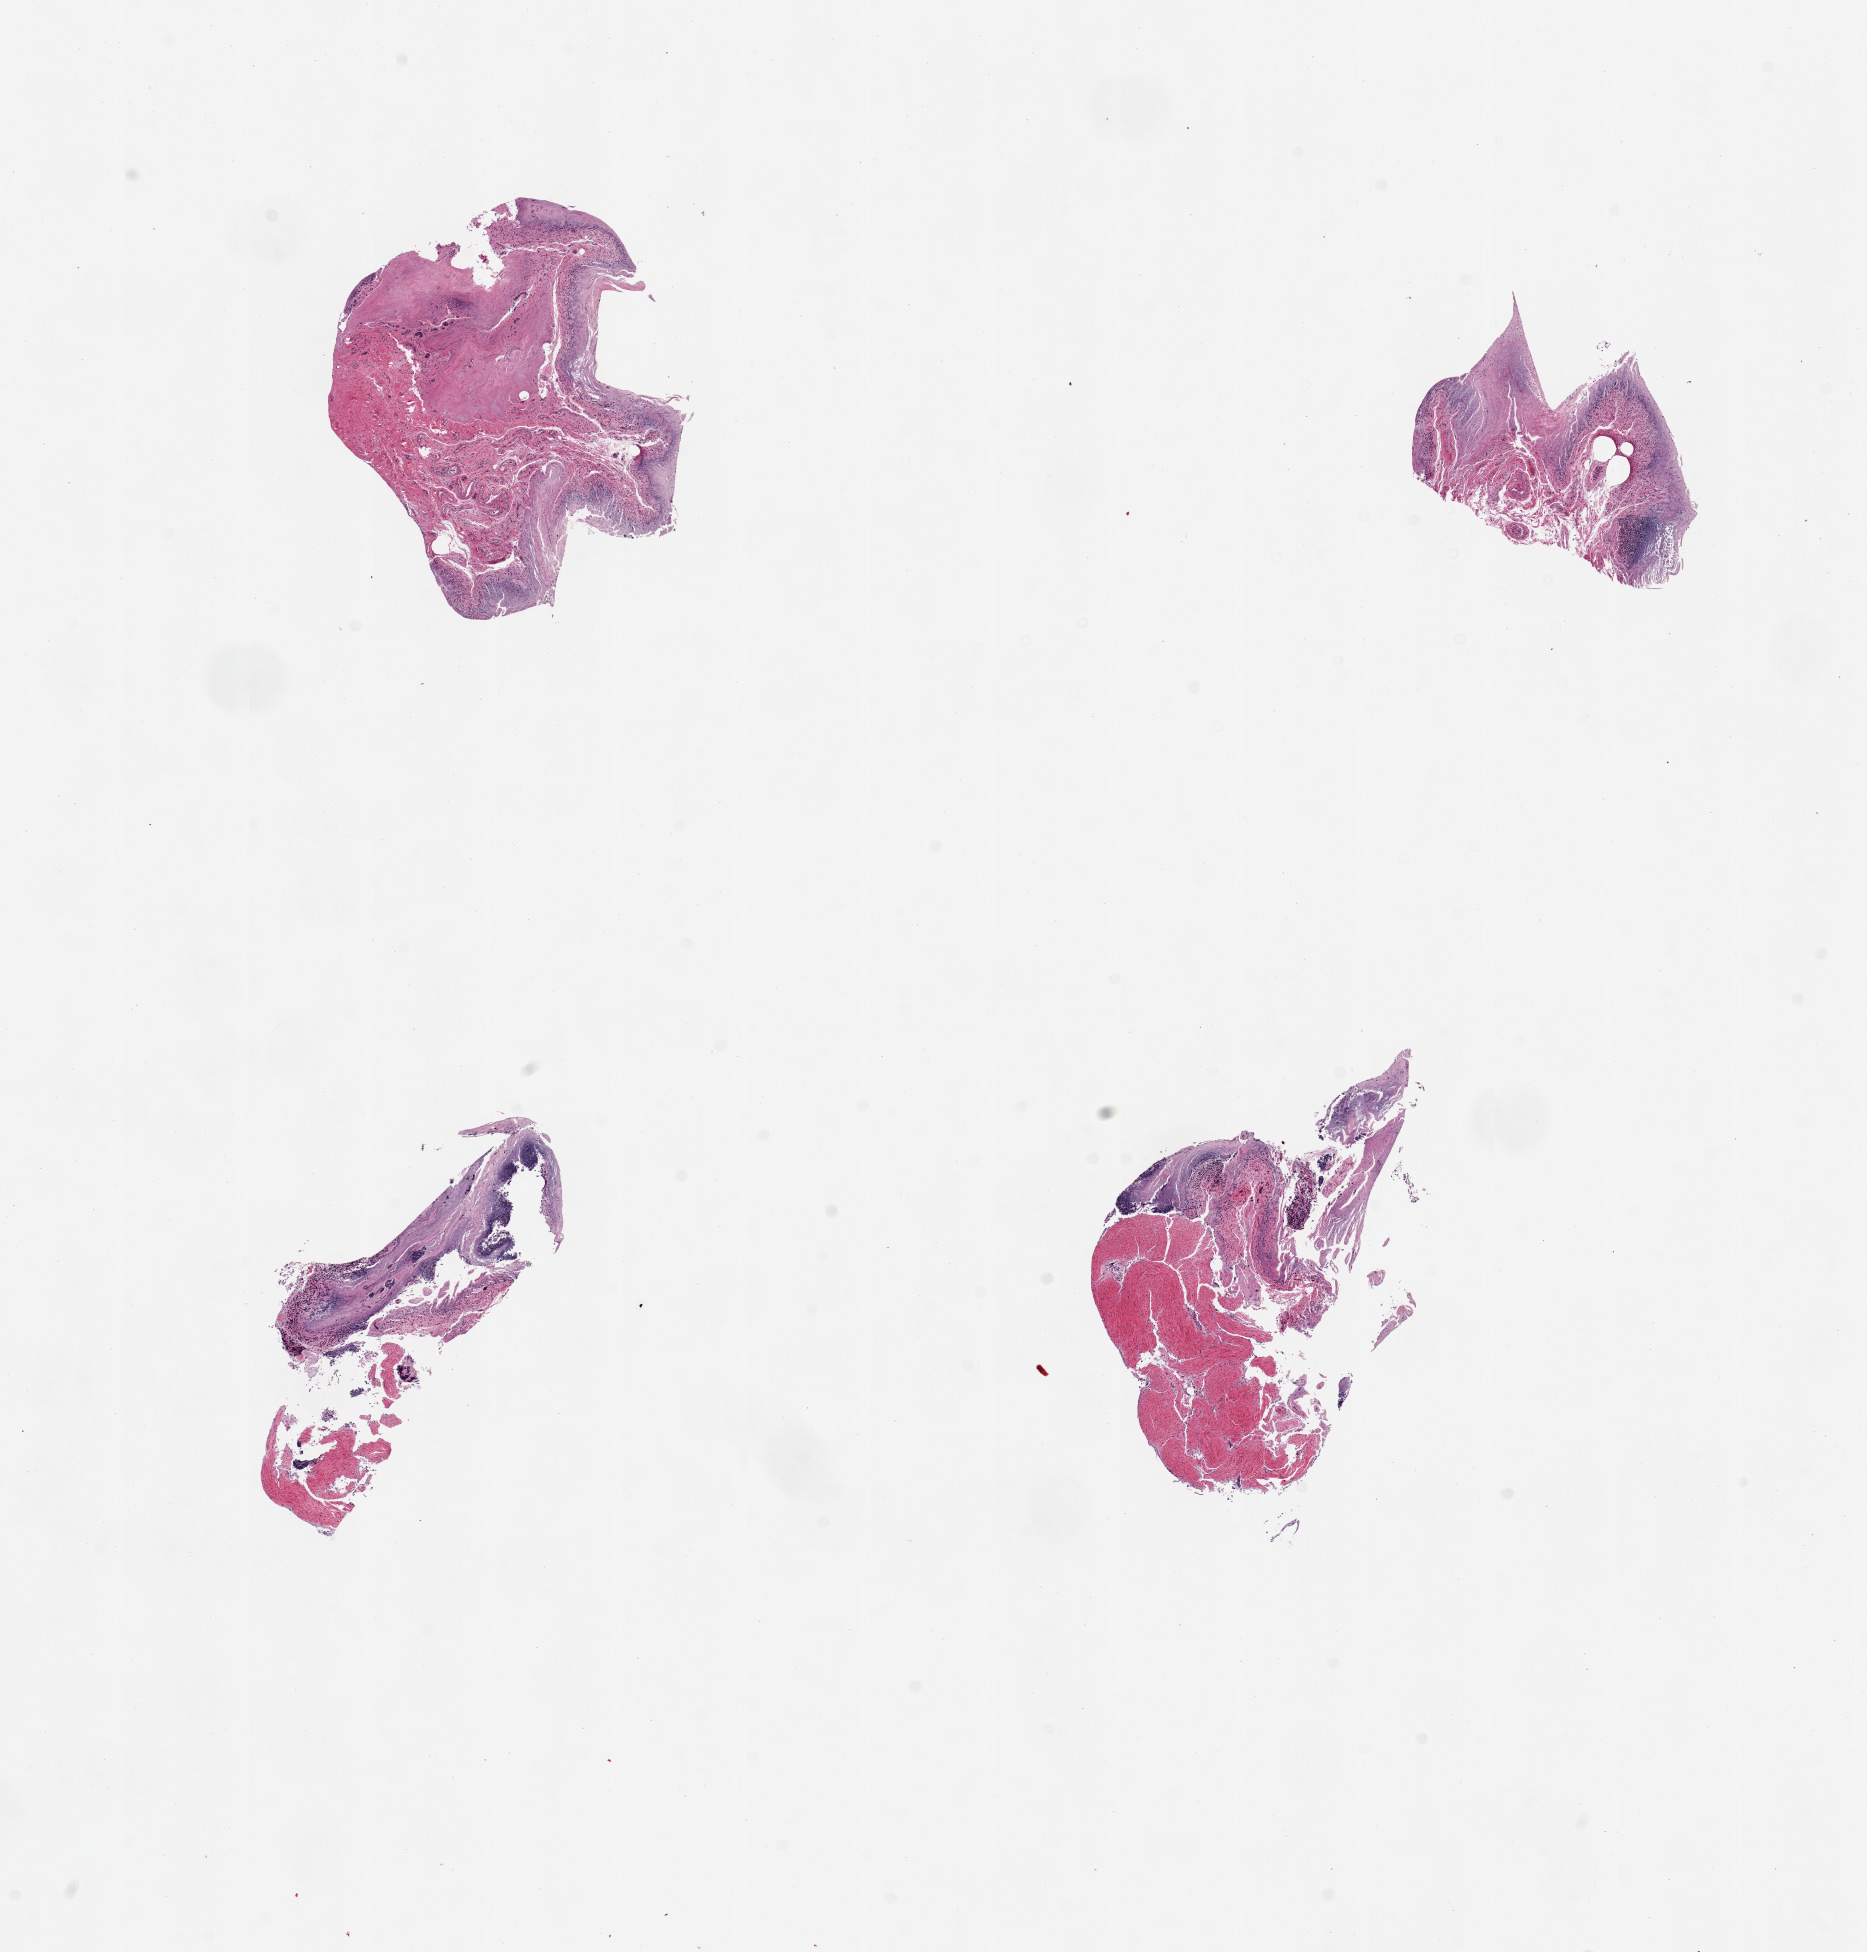
Haematoxylin and eosin whole-slide image, brightfield — low-resolution overview of the scanned area, about 14.8 x 15.4 mm; PAXgene-fixed, paraffin-embedded tissue; target tissue: ileum; tissue donor sample. Donor sex: male.
Review note (as recorded): 4 pieces, glandular mucosa totally autolyzed, residual lymphoid aggregates are ~10% remaining tissue.